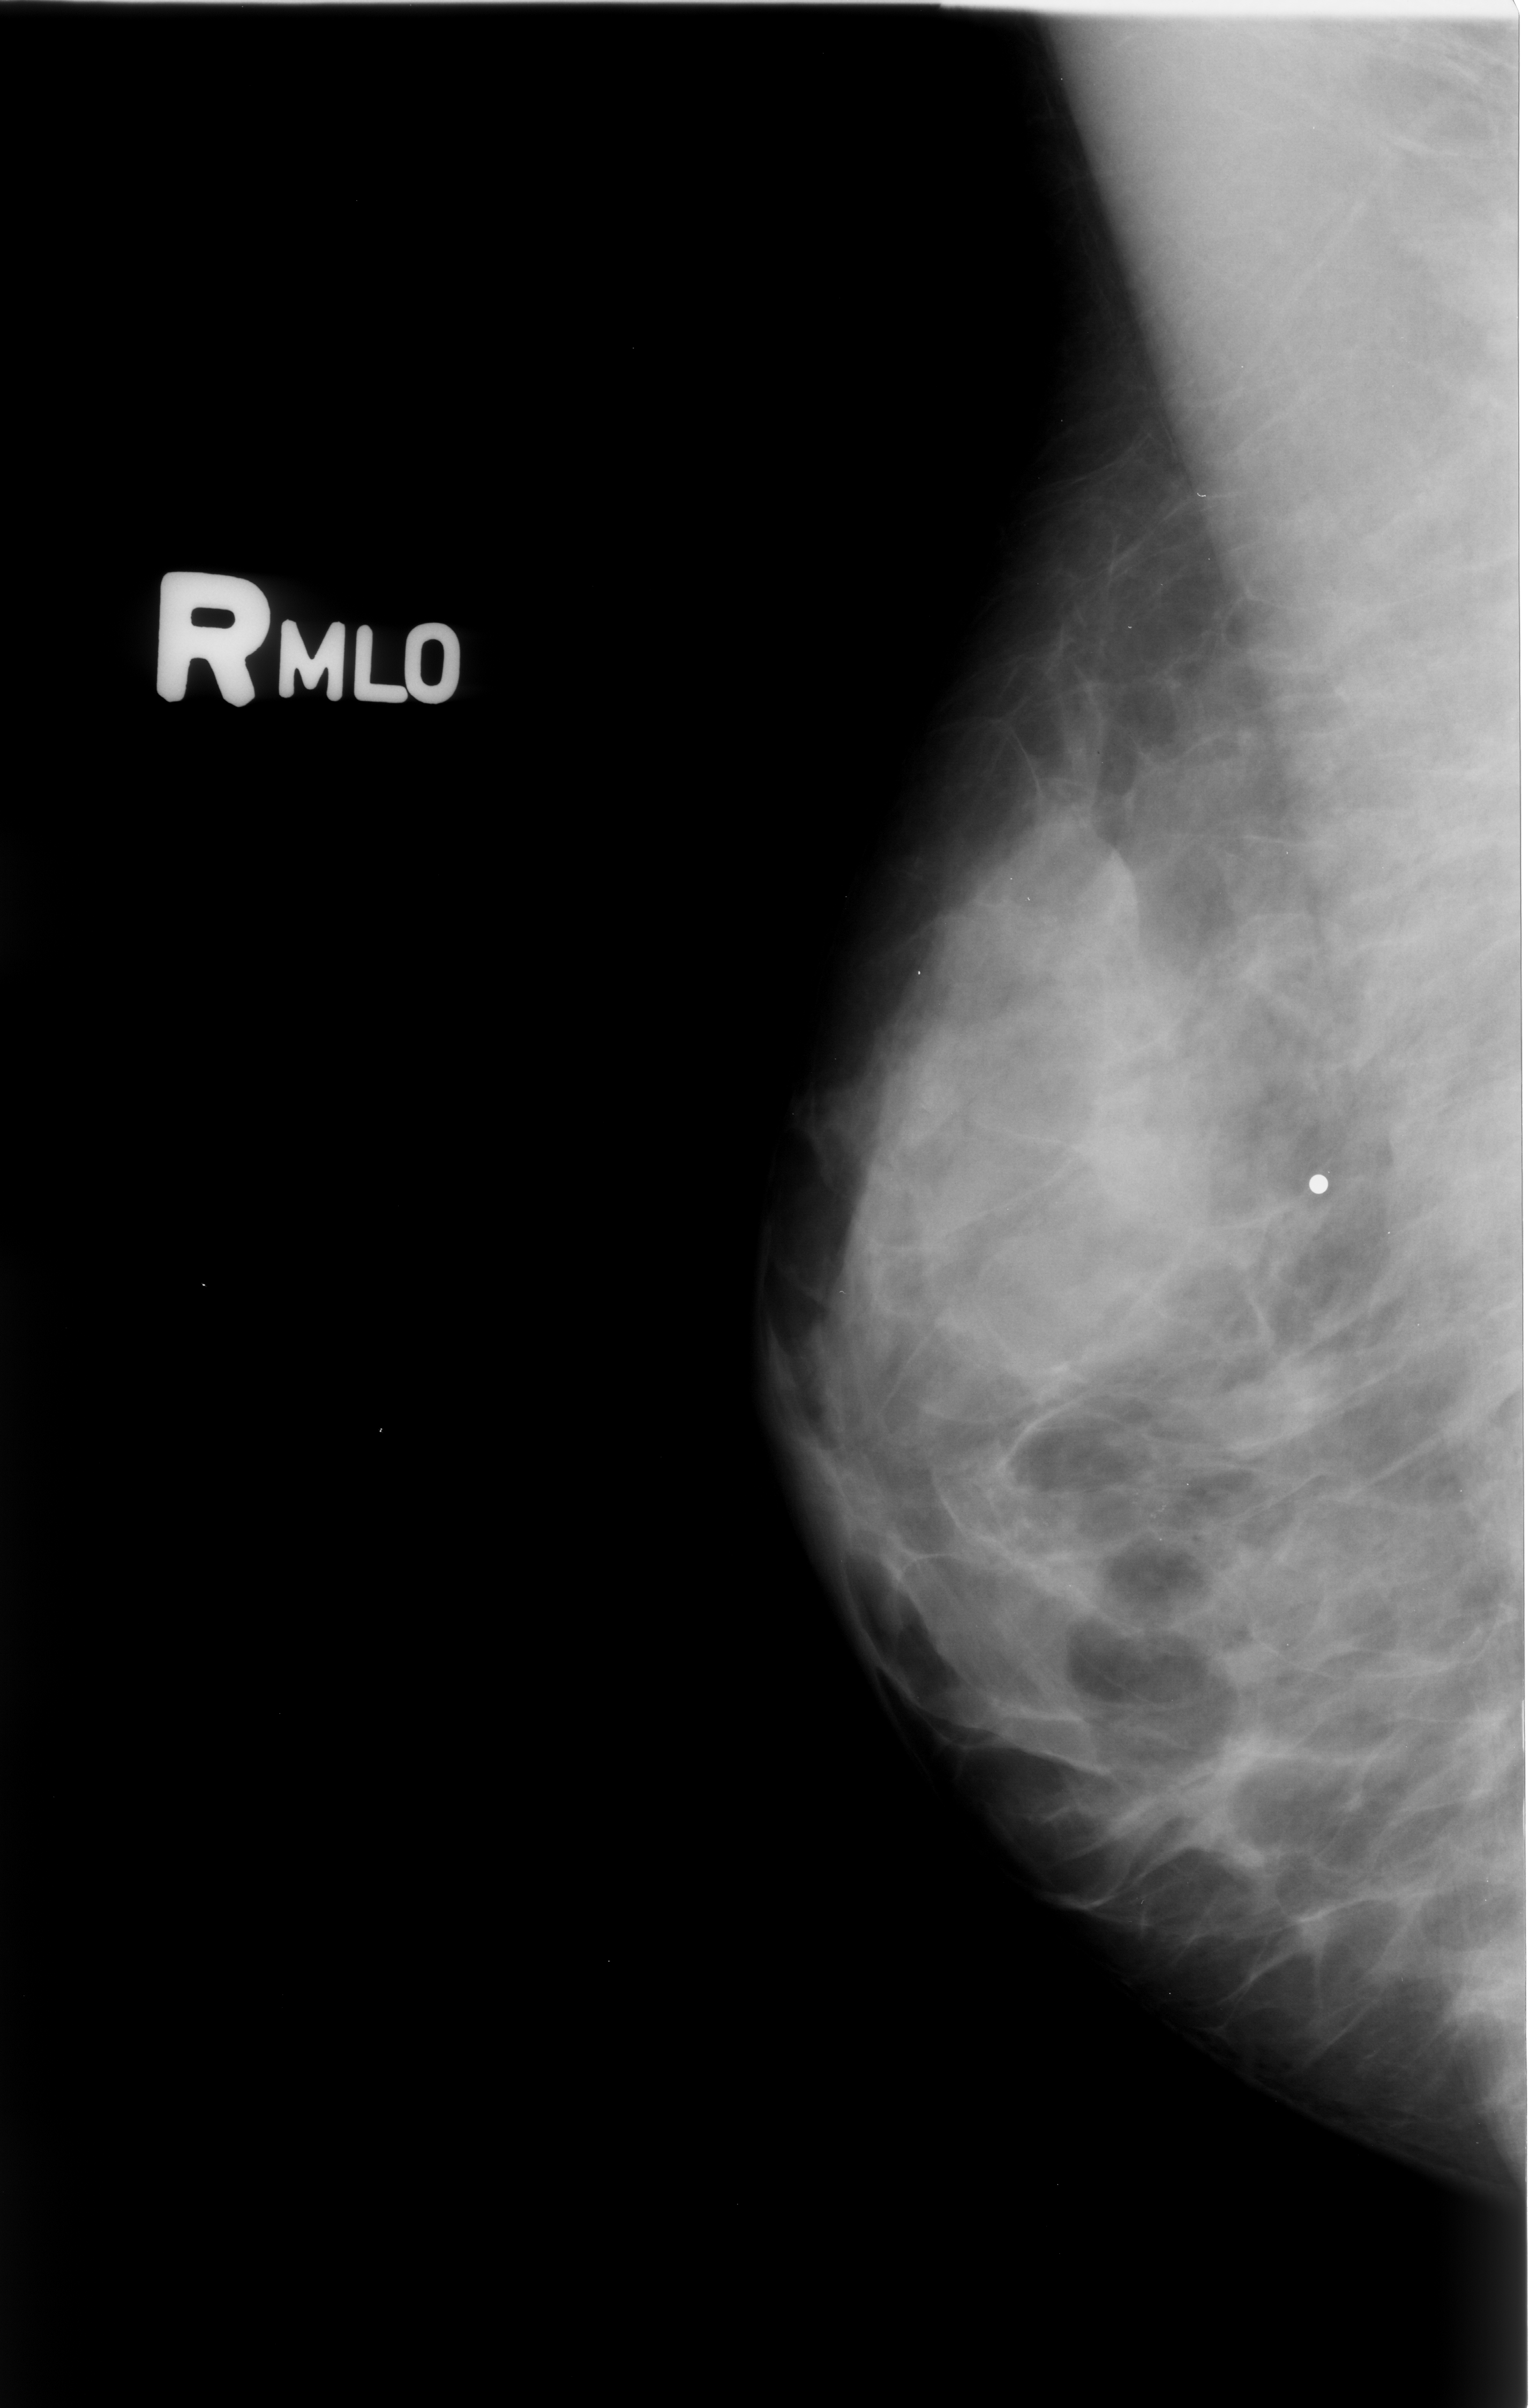
Mammogram (digitized film); right breast; MLO view; BI-RADS breast density category 3 (scale 1–4); 1530 × 2408 image matrix.
Expert-marked regions of interest on this film, with their recorded descriptors:
- calcifications, morphology pleomorphic, distribution clustered; BI-RADS assessment category 4; pathology (as recorded): benign: bounding box (x1, y1, x2, y2) in pixels: (1067, 1426, 1235, 1582)